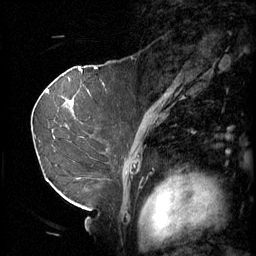
Breast MRI (dynamic contrast-enhanced), one sagittal slice. Slice 36 of 60 in the series (ordered by position). 3 images stored at this slice position (order not interpretable as contrast timing). 1.5 T. TE 4.2 ms, TR 11 ms. 256 × 256 image matrix, field of view 220 × 220 mm. Patient: female, 69 years.
Outlined on this slice (semi-automatically segmented with operator editing):
- analysis volume of interest (the breast-tissue region the enhancement analysis was run in; not a lesion): bounding box [x1, y1, x2, y2] px = [36, 88, 108, 189]
- tumour enhancement mask (voxels above the 70 % enhancement threshold inside the analysis volume of interest): [70, 102, 73, 109]